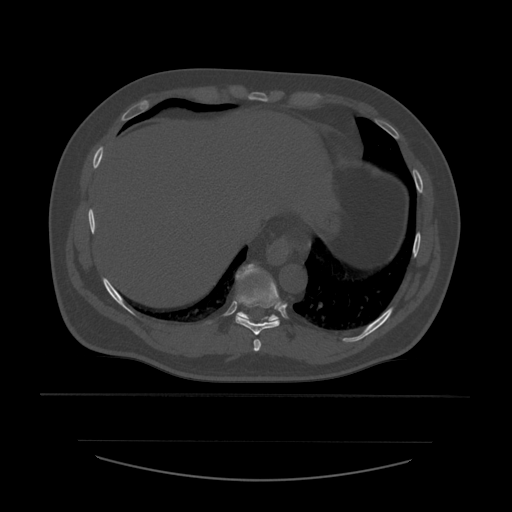
CT including the spine, one axial slice. Position 312 of 532 along the scan axis. Reconstruction kernel STANDARD. Bone window (W 1800 / L 400 HU). 1.25 mm slice thickness. 512 × 512 image matrix, field of view 441 × 441 mm. Patient age 44 years. From the clinical record (not read from this slice): primary cancer: soft tissue sarcoma.
Annotated regions visible in this slice (semi-automatically segmented with operator editing):
- T10 vertebra: bounding box <237,264,279,321> (left, top, right, bottom; pixels)
- T8 vertebra: <254,340,262,353>
- T9 vertebra: <236,272,282,336>